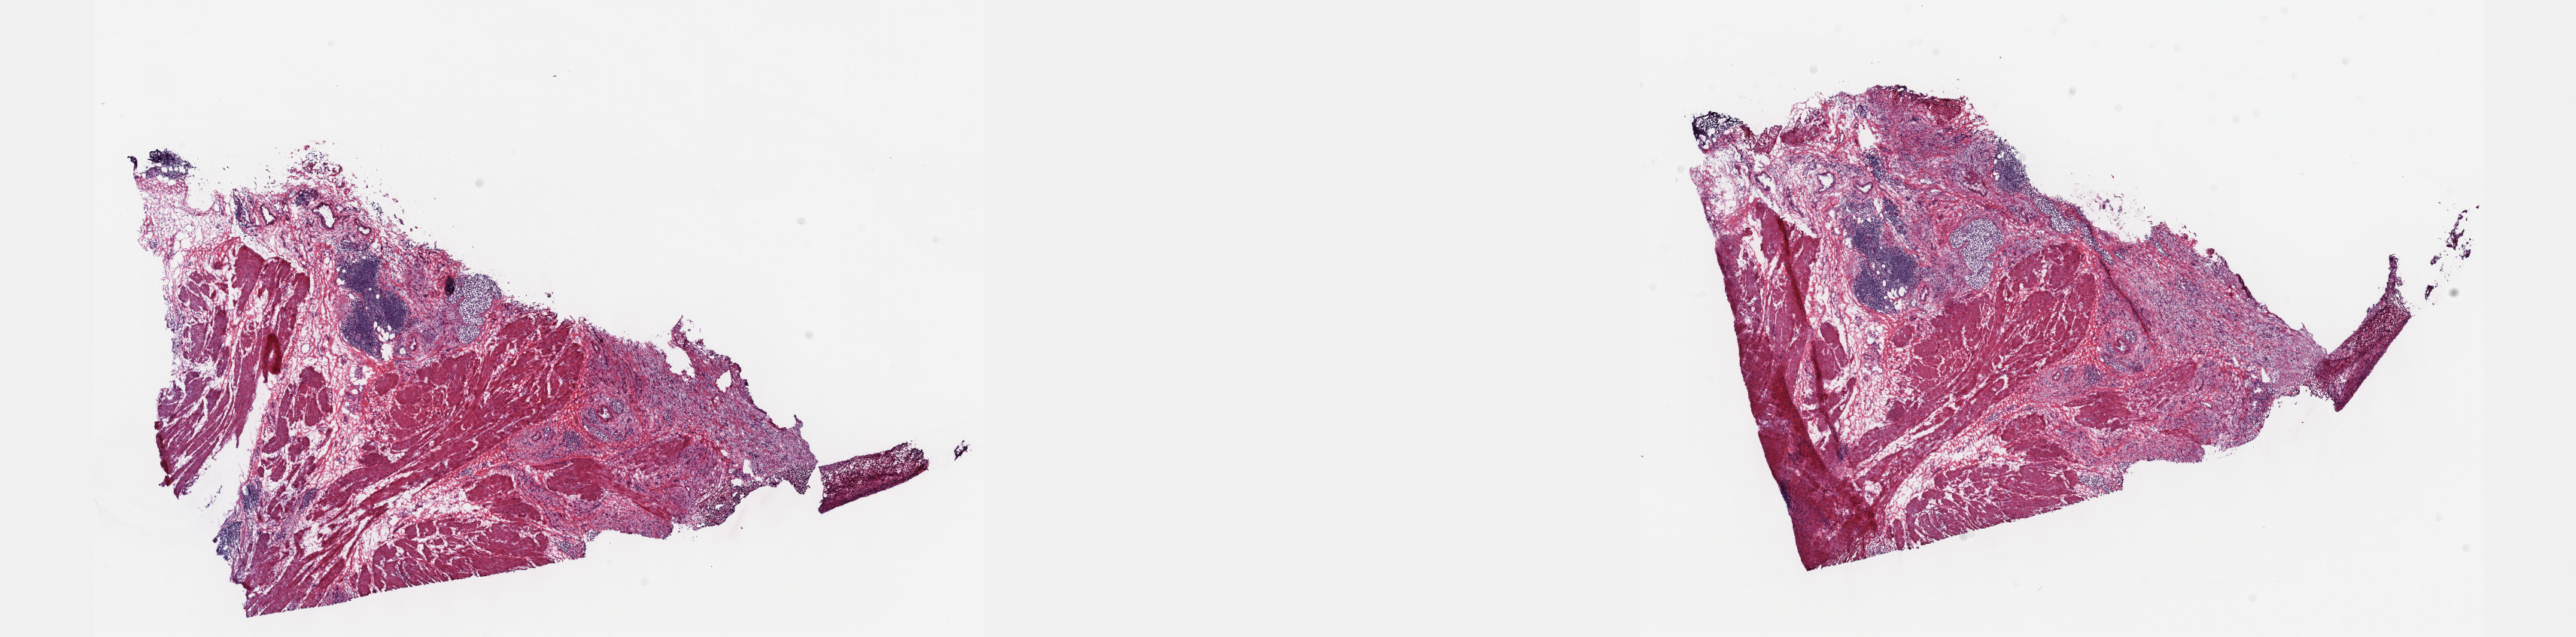
Digitized Hematoxylin and eosin (H&E) stained tissue section (whole slide), a low-resolution overview of the entire scanned area, about 27.7 x 6.8 mm, frozen section from the top of the tissue portion, bladder, primary tumour sample. Male, age 69 years at initial diagnosis. Slide review estimates, as recorded: tumour cells 60%, tumour nuclei 60%.
Pathologic diagnosis: Transitional cell carcinoma.